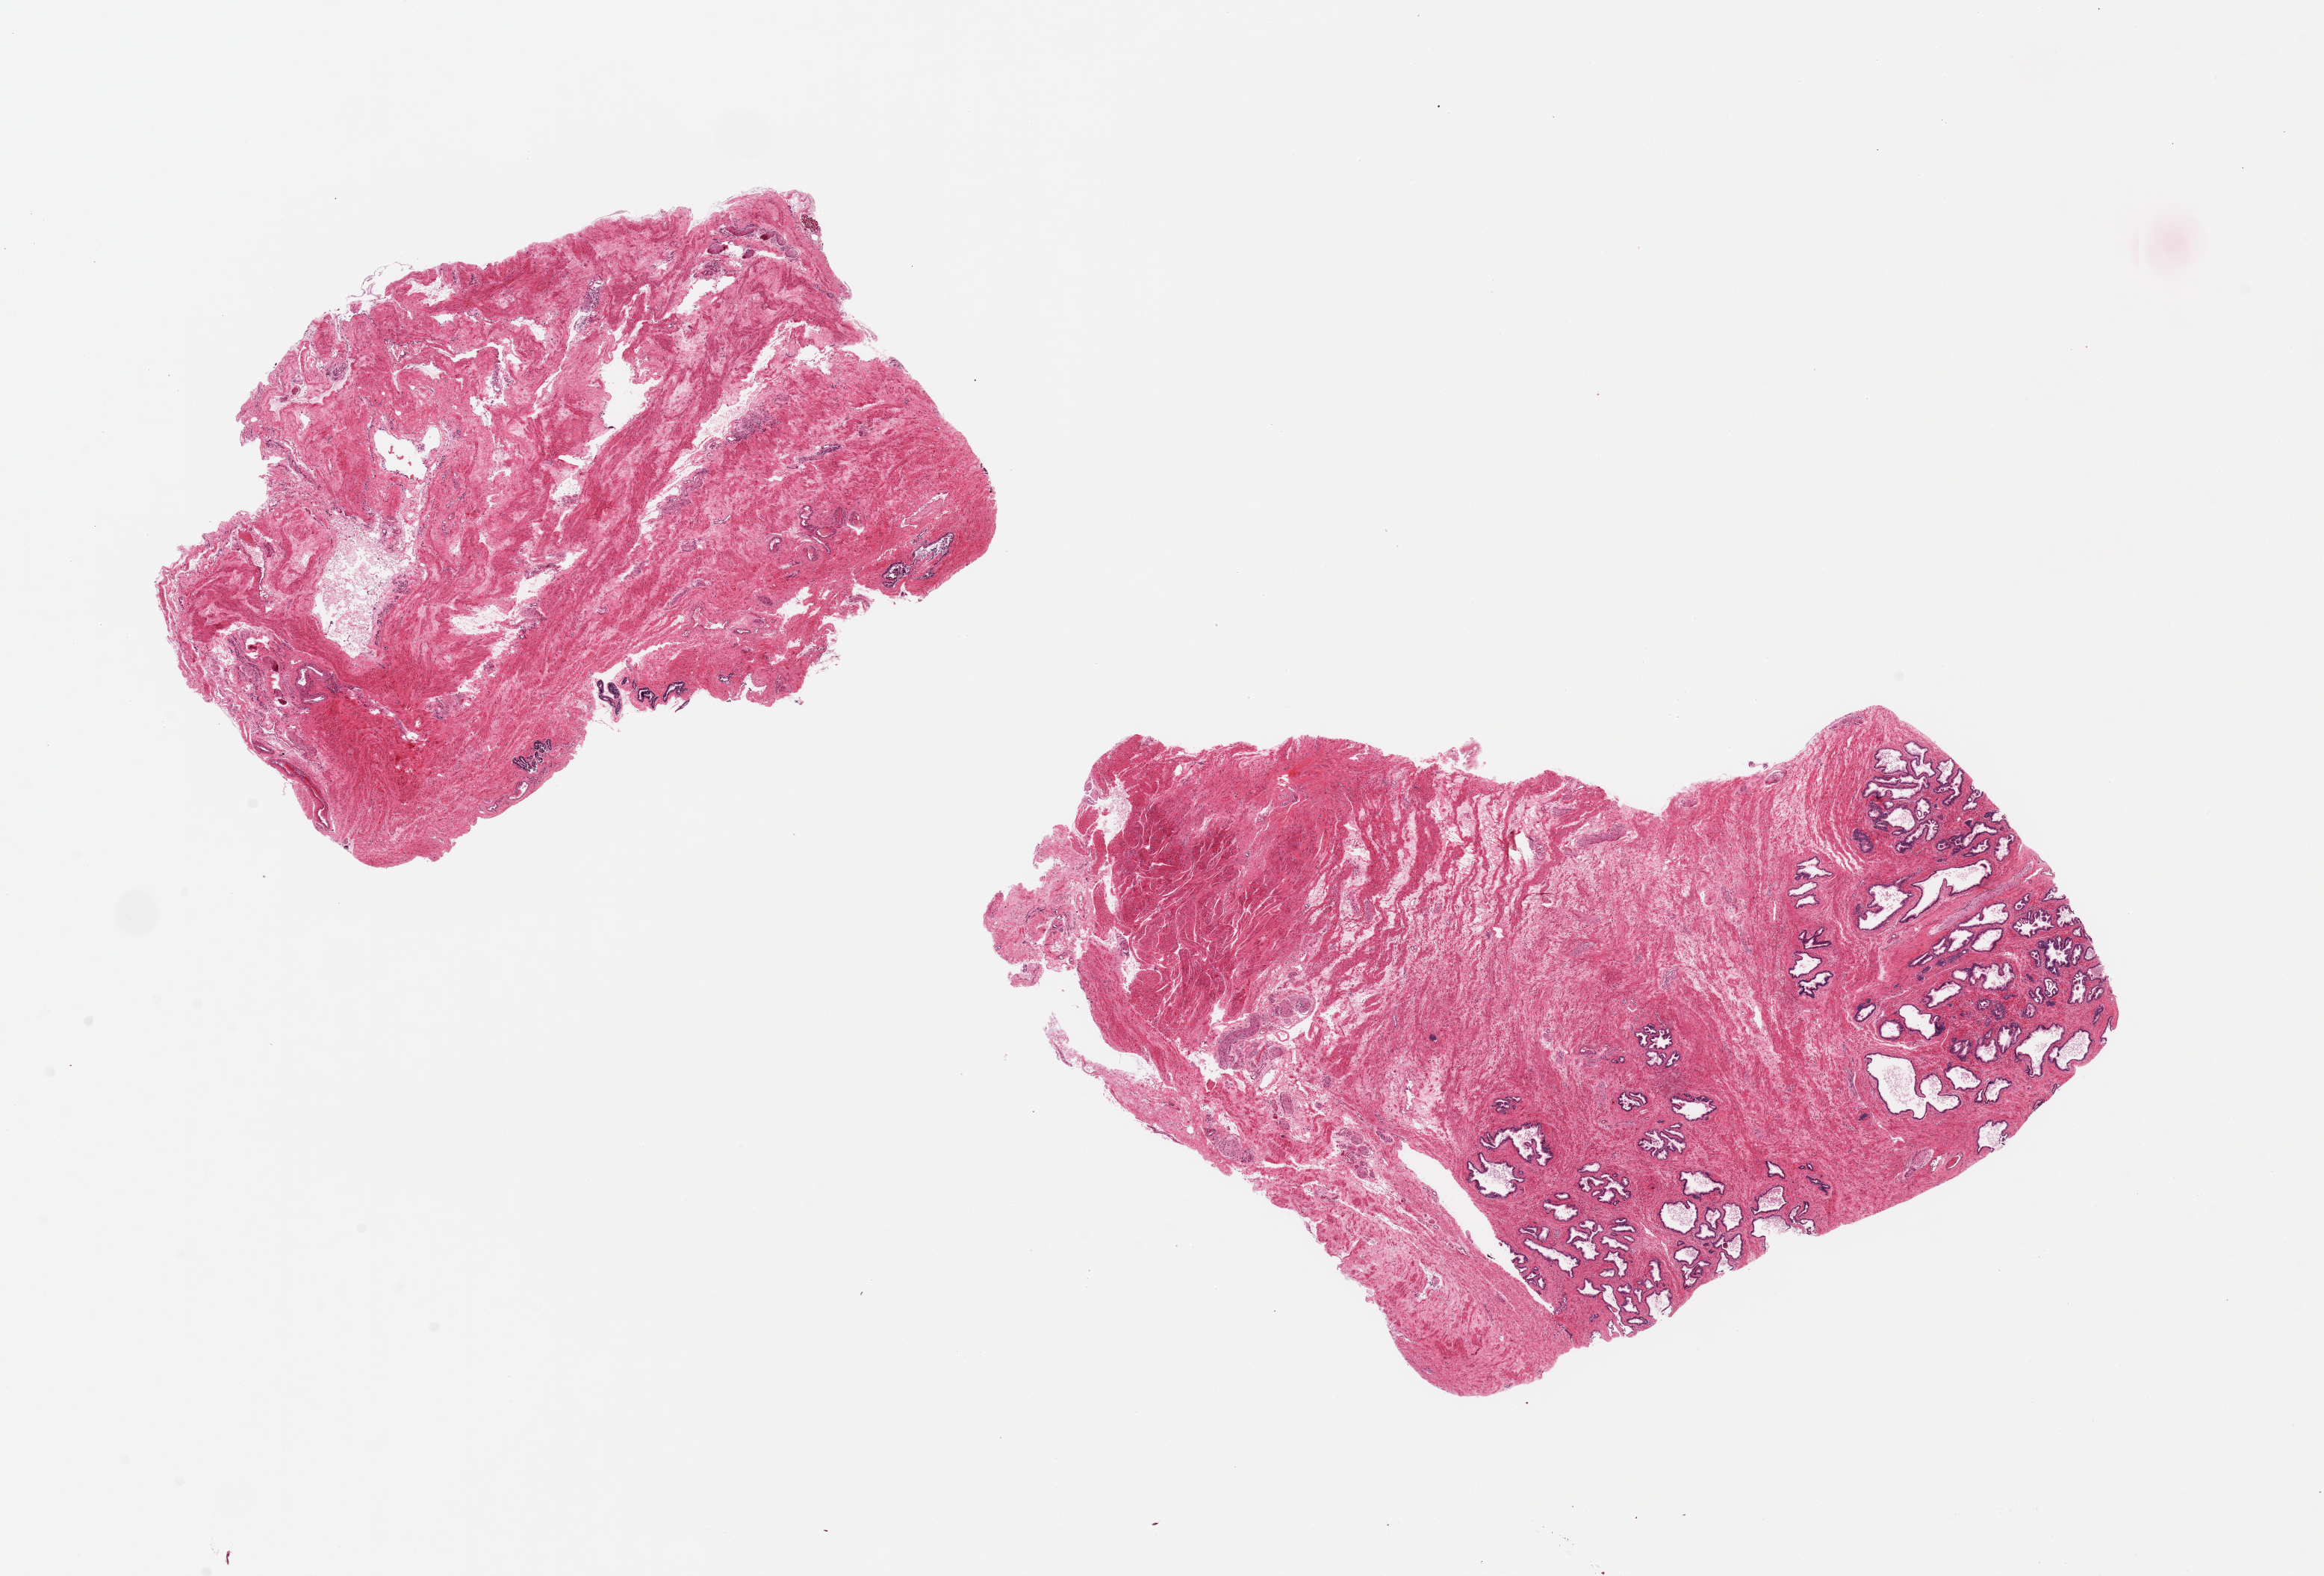
H&E whole-slide image, whole scanned area (about 24.6 x 16.7 mm) shown as a low-resolution overview, PAXgene-fixed paraffin-embedded (PFPE) section, target tissue: prostate, tissue donor sample. Male donor.
* review note (as recorded): 2 pieces ~8x7mm, one aliquot with minimal glands, mainly stroma